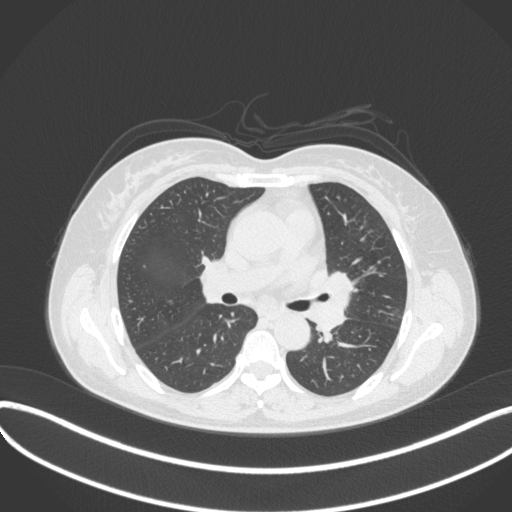
Chest CT, one axial slice; reconstruction kernel B31f; lung window (W 1500 / L -600 HU); 512 × 512 image matrix, field of view 400 × 400 mm. Patient: female, 54 years. Case-level facts recorded for this patient, not image findings: clinical TNM (as recorded): T2a N1 M0; histopathological grade: G3.
Structures marked on this image (bounding box drawn by a radiologist):
- lung tumour (recorded histology: small cell carcinoma): bounding box <309,268,355,333> (left, top, right, bottom; pixels)